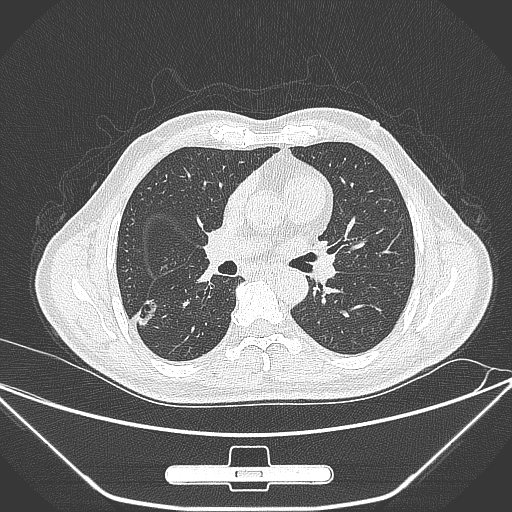
Chest CT, one axial slice; position 155 of 309 along the scan axis; lung window (W 1500 / L -600 HU); 1 mm slice thickness; 512 × 512 image matrix. Male patient, age 71 years. From the clinical record (not read from this slice): clinical TNM (as recorded): T1c N0 M0.
Annotated regions visible in this slice (rectangle marked by the reading radiologist):
- lung tumour (recorded histology: adenocarcinoma): box from (x=134, y=295) to (x=166, y=336) px